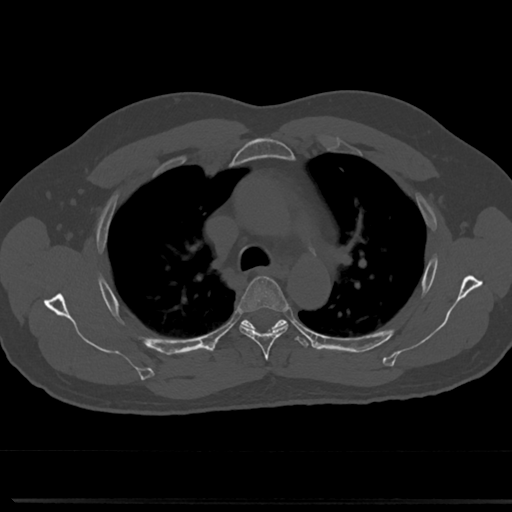
CT including the spine, one axial slice; slice 531 of 817 in the series (ordered by position); reconstruction kernel Br40s/3; 120 kVp; bone window (W 1800 / L 400 HU); 0.5 mm slice thickness; 512 × 512 image matrix. Male patient, age 61 years. Case-level facts recorded for this patient, not image findings: primary cancer: prostate.
Annotated regions visible in this slice (semi-automatic segmentation, software-assisted and operator-edited):
- T4 vertebra: box from (x=238, y=276) to (x=290, y=356) px
- T5 vertebra: (x=244, y=320)–(x=284, y=327)